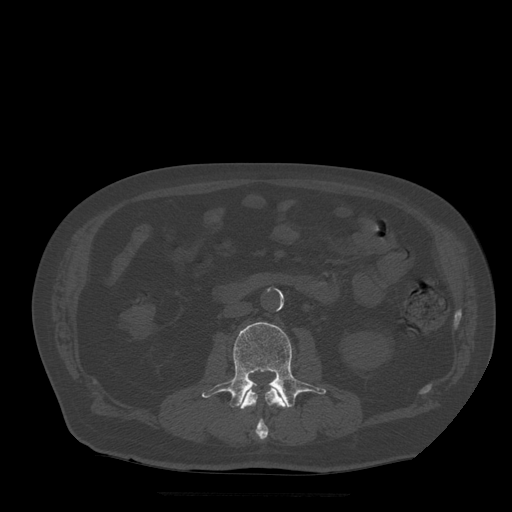
CT including the spine, one axial slice; position 148 of 522 along the scan axis; bone window (W 1800 / L 400 HU); 1.25 mm slice thickness; 512 × 512 image matrix. Patient age 72 years. From the clinical record (not read from this slice): primary cancer: prostate.
Outlined on this slice (semi-automatic segmentation, software-assisted and operator-edited):
- L2 vertebra: bounding box (x1, y1, x2, y2) in pixels: (238, 384, 288, 440)
- L3 vertebra: (202, 322, 326, 408)